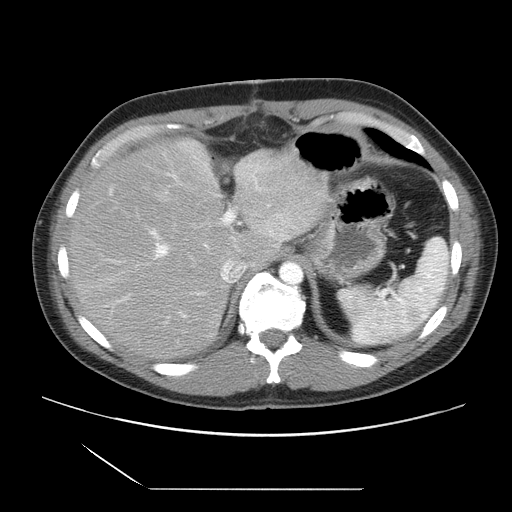
Contrast-enhanced abdominal CT, one axial slice. Position 21 of 39 along the scan axis. Intravenous contrast given. Soft-tissue window (W 400 / L 40 HU). 5 mm slice thickness. 512 × 512 image matrix. Male patient, age 39 years. From the clinical record (not read from this slice): diagnosis: colorectal cancer liver metastases, imaged before liver resection; multiple liver metastases: yes; largest metastasis: 1.3 cm; chemotherapy before resection: yes.
Structures marked on this image (manually delineated by an expert):
- hepatic veins: box from (x=199, y=260) to (x=247, y=308) px
- liver: (x=69, y=141)–(x=327, y=360)
- planned liver remnant (the part of the liver to remain after resection): (x=113, y=141)–(x=326, y=266)
- portal vein (with intrahepatic branches): (x=103, y=164)–(x=264, y=324)